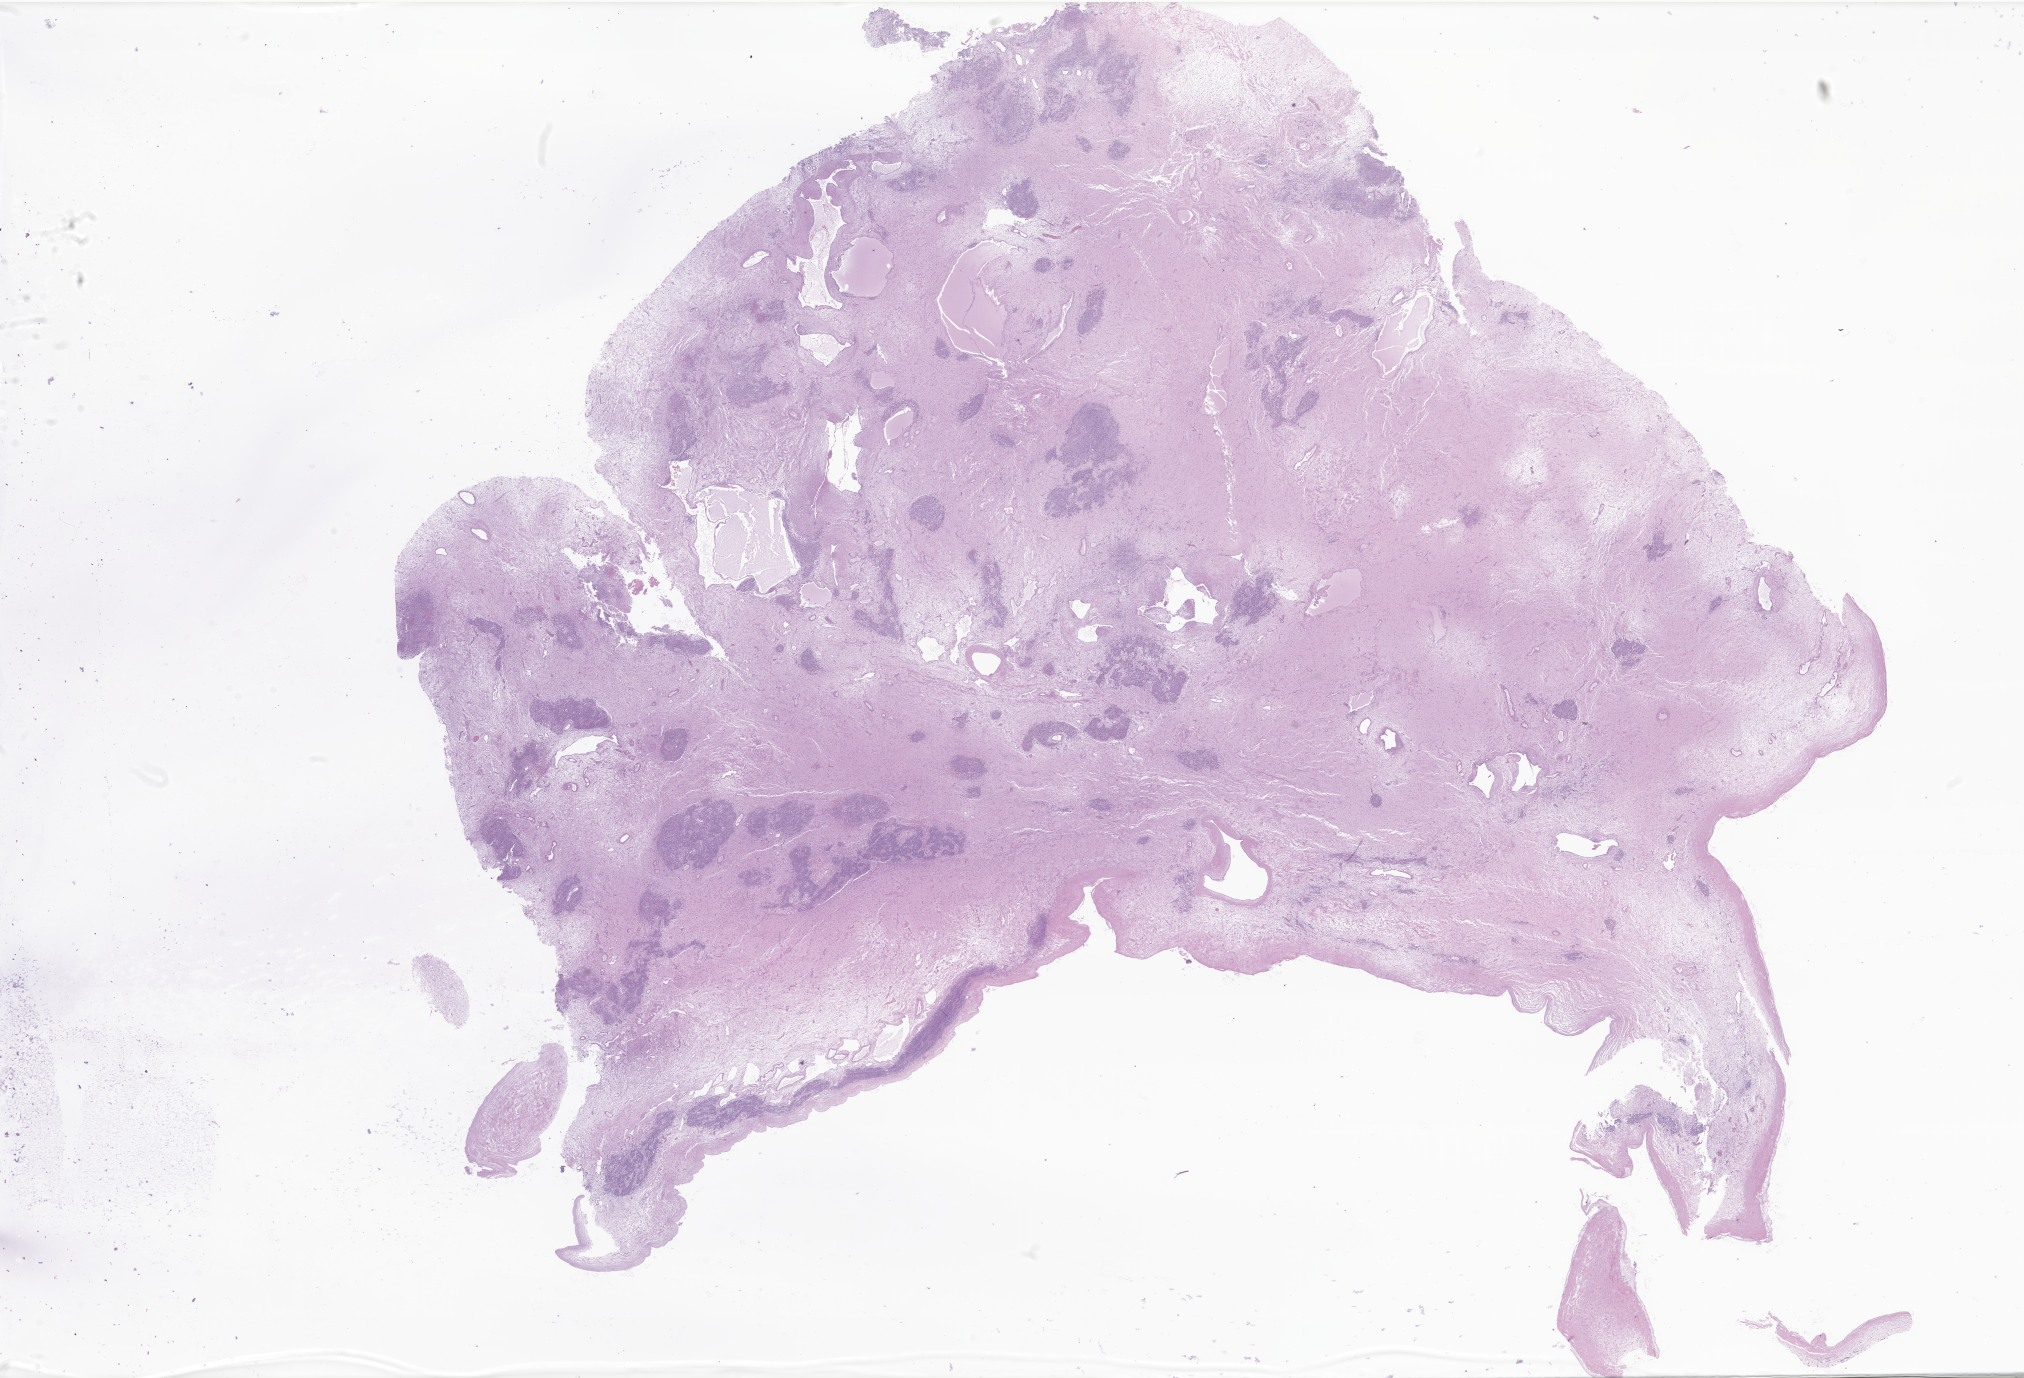
Digitized haematoxylin and eosin-stained section of tumor tissue from the ovary — shown as a low-resolution overview of the whole scanned area (about 34.1 x 23.2 mm), FFPE section. Female patient, age 174 months (14 years 6 months).
• diagnosis: Sertoli-Leydig cell tumor of intermediate differentiation, NOS